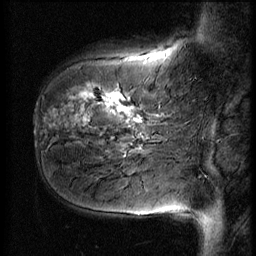
Breast MRI (dynamic contrast-enhanced), one sagittal slice; slice 14 of 56 in the series (ordered by position); 3 images stored at this slice position (order not interpretable as contrast timing); 1.5 T; TE 4.2 ms, TR 9 ms; 256 × 256 image matrix, field of view 180 × 180 mm. Patient: female, 51 years. Case-level facts recorded for this patient, not image findings: setting: breast cancer imaged before/during neoadjuvant chemotherapy; receptor status: HR-positive, HER2-negative.
Annotated regions visible in this slice (semi-automatic segmentation, software-assisted and operator-edited):
- analysis volume of interest (the breast-tissue region the enhancement analysis was run in; not a lesion): bounding box <41,58,167,161> (left, top, right, bottom; pixels)
- tumour enhancement mask (voxels above the 140 % enhancement threshold inside the analysis volume of interest): <71,90,149,152>